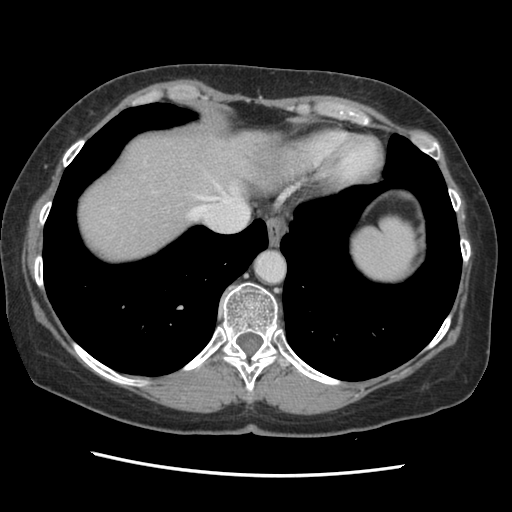
Contrast-enhanced abdominal CT, one axial slice; position 121 of 141 along the scan axis; soft-tissue window (W 400 / L 40 HU); 512 × 512 image matrix. Female patient, age 61 years. From the clinical record (not read from this slice): diagnosis: colorectal cancer liver metastases, imaged before liver resection; multiple liver metastases: no; largest metastasis: 2.4 cm; disease in both lobes: no.
Annotated regions visible in this slice (expert manual segmentation):
- hepatic veins: bounding box <188,183,242,219> (left, top, right, bottom; pixels)
- liver: <76,129,273,263>
- planned liver remnant (the part of the liver to remain after resection): <77,130,280,264>